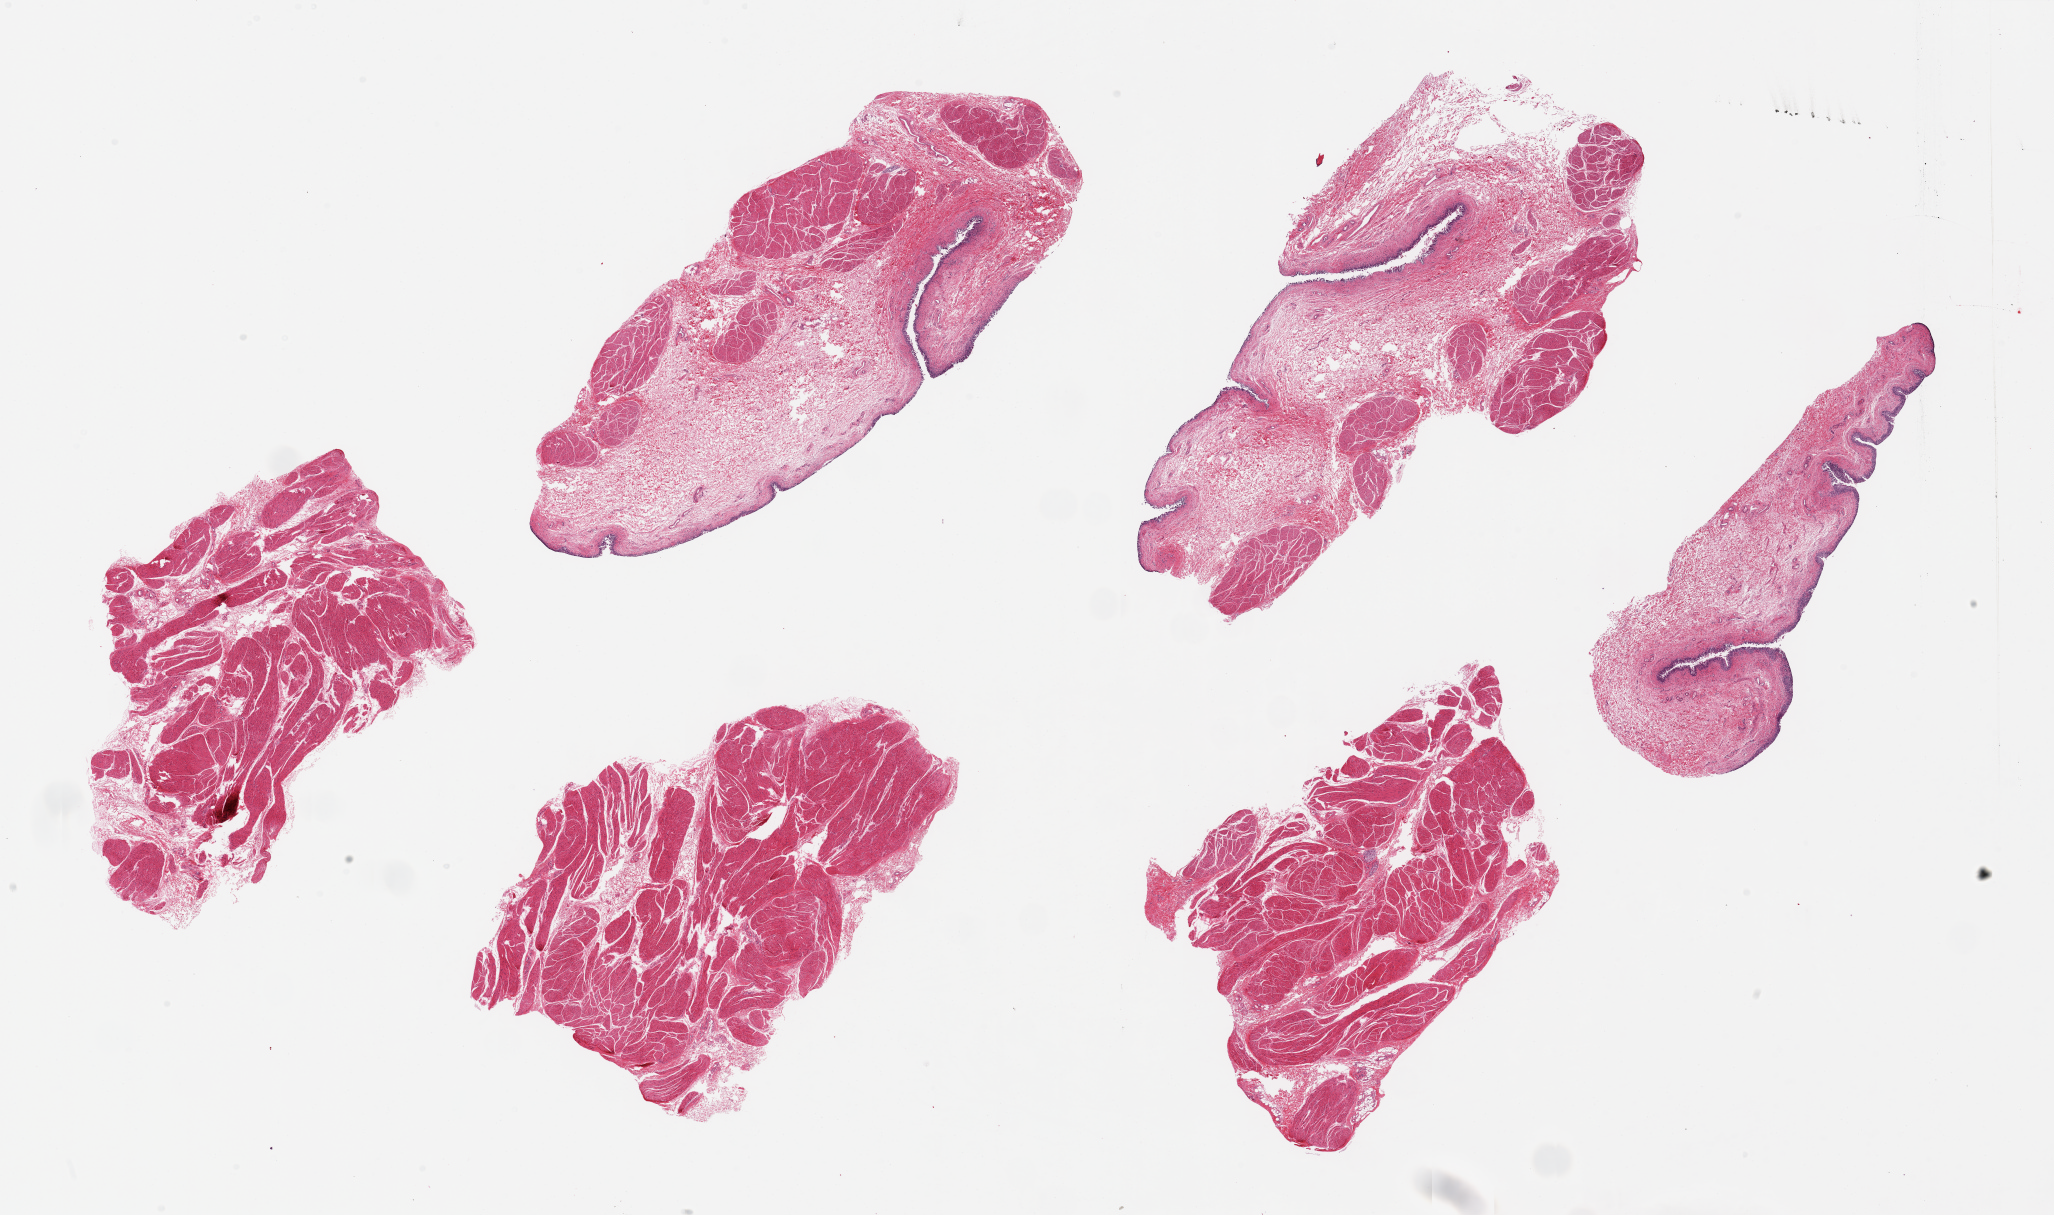
Hematoxylin and eosin (H&E) whole-slide image, brightfield — shown as a low-resolution overview of the whole scanned area (about 32.5 x 19.2 mm), PAXgene-fixed paraffin-embedded (PFPE) section, target tissue: urinary bladder, tissue donor sample.
• reviewer comment on this tissue sample: 6 pieces up to 10x5 mm; 3 have partially sloughed epithelium; 3 have only muscular wall